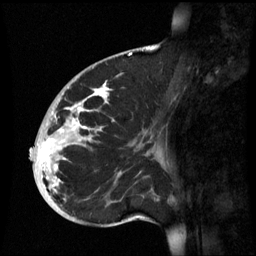
Breast MRI (dynamic contrast-enhanced), one sagittal slice. Position 25 of 60 along the scan axis. Dynamic contrast-enhanced series, image 2 of 3 at this slice position (ordered by acquisition). 1.5 T. TE 4.2 ms, TR 8.9 ms. 256 × 256 image matrix. Female patient, age 35 years. From the clinical record (not read from this slice): setting: breast cancer imaged before/during neoadjuvant chemotherapy; receptor status: HR-positive, HER2-negative.
Structures marked on this image (semi-automatically segmented with operator editing):
- analysis volume of interest (the breast-tissue region the enhancement analysis was run in; not a lesion): bounding box <32,74,164,221> (left, top, right, bottom; pixels)
- tumour enhancement mask (voxels above the 70 % enhancement threshold inside the analysis volume of interest): <38,82,110,189>